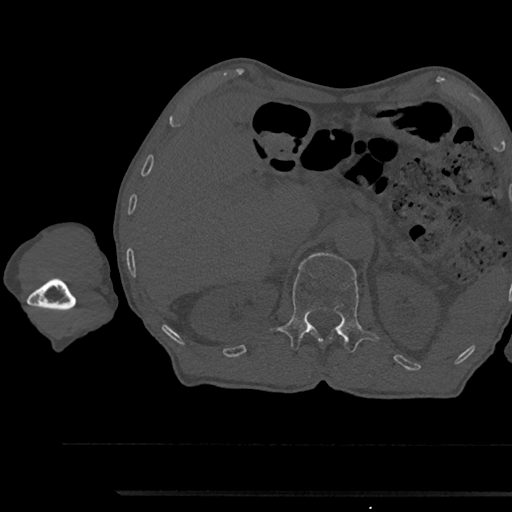
CT including the spine, one axial slice. Bone window (W 1800 / L 400 HU). 512 × 512 image matrix. Male patient, age 79 years. Case-level facts recorded for this patient, not image findings: primary cancer: prostate.
Outlined on this slice (semi-automatically segmented with operator editing):
- L1 vertebra: bounding box <269,252,379,352> (left, top, right, bottom; pixels)